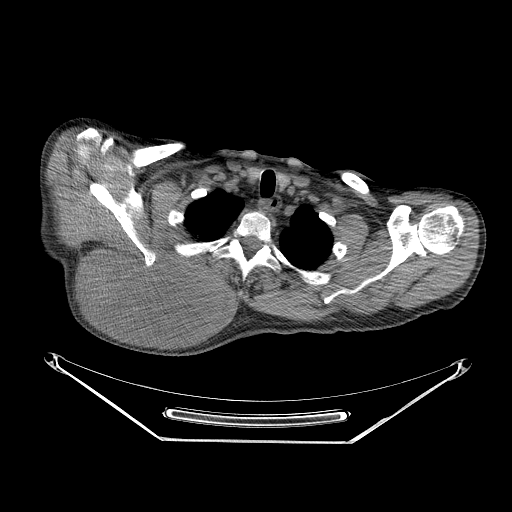
CT of an extremity soft-tissue mass (from a PET/CT study), one axial slice. Slice 203 of 267 in the series (ordered by position). Reconstruction kernel STANDARD. Soft-tissue window (W 400 / L 40 HU). 3.75 mm slice thickness. 512 × 512 image matrix, field of view 500 × 500 mm. Male patient. Case-level facts recorded for this patient, not image findings: histological type: pleiomorphic spindle cell undifferentiated; grade: high; site of the primary tumour: right parascapusular.
Annotated regions visible in this slice (expert contour drawn on MRI and transferred to this co-registered scan by the dataset authors):
- gross tumour volume including surrounding oedema: box from (x=80, y=244) to (x=234, y=332) px
- gross tumour volume (mass): (x=82, y=249)–(x=222, y=330)